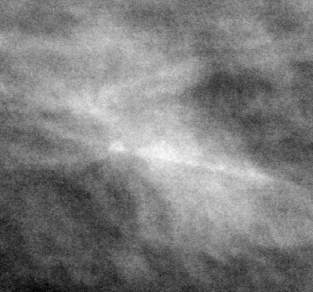
Region of interest cut from a scanned film mammogram (one marked finding), left breast, MLO view, BI-RADS breast density category 1 (scale 1–4).
- Mass, shape oval, margins circumscribed; BI-RADS assessment category 3; subtlety rating 3 on a 1 (subtle) to 5 (obvious) scale; benign without callback (not worked up further).